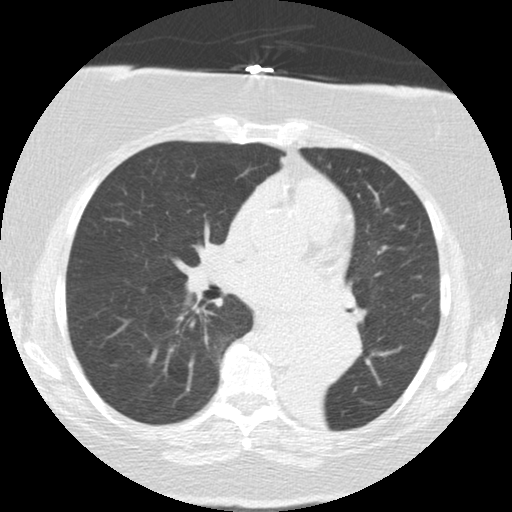
Low-dose screening chest CT, one axial slice; 120 kVp; lung window (W 1500 / L -600 HU); 2.5 mm slice thickness; 512 × 512 image matrix, field of view 309 × 309 mm.
Structures marked on this image (expert manual segmentation):
- lesion 2 (tumor, mediastinum): bounding box [x1, y1, x2, y2] px = [296, 309, 366, 387]